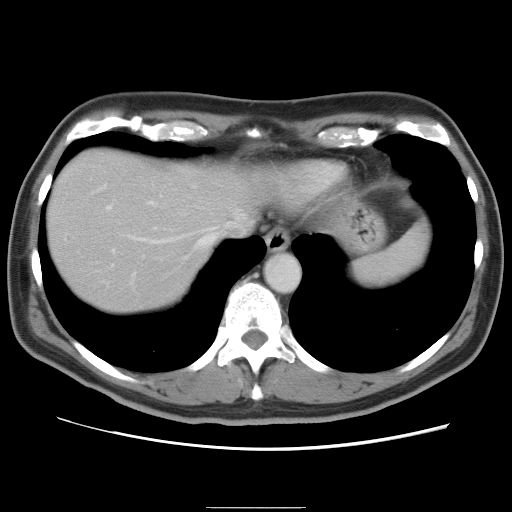
Contrast-enhanced abdominal CT, one axial slice. Position 71 of 87 along the scan axis. 120 kVp. Intravenous contrast given. Soft-tissue window (W 400 / L 40 HU). 5 mm slice thickness. 512 × 512 image matrix, field of view 363 × 363 mm. Male patient, age 63 years. Case-level facts recorded for this patient, not image findings: diagnosis: colorectal cancer liver metastases, imaged before liver resection; multiple liver metastases: no; largest metastasis: 9 cm.
Structures marked on this image (outlined manually by an expert reader):
- hepatic veins: box from (x=96, y=184) to (x=245, y=259) px
- liver: (x=46, y=149)–(x=252, y=315)
- planned liver remnant (the part of the liver to remain after resection): (x=47, y=169)–(x=210, y=315)
- portal vein (with intrahepatic branches): (x=104, y=203)–(x=158, y=285)